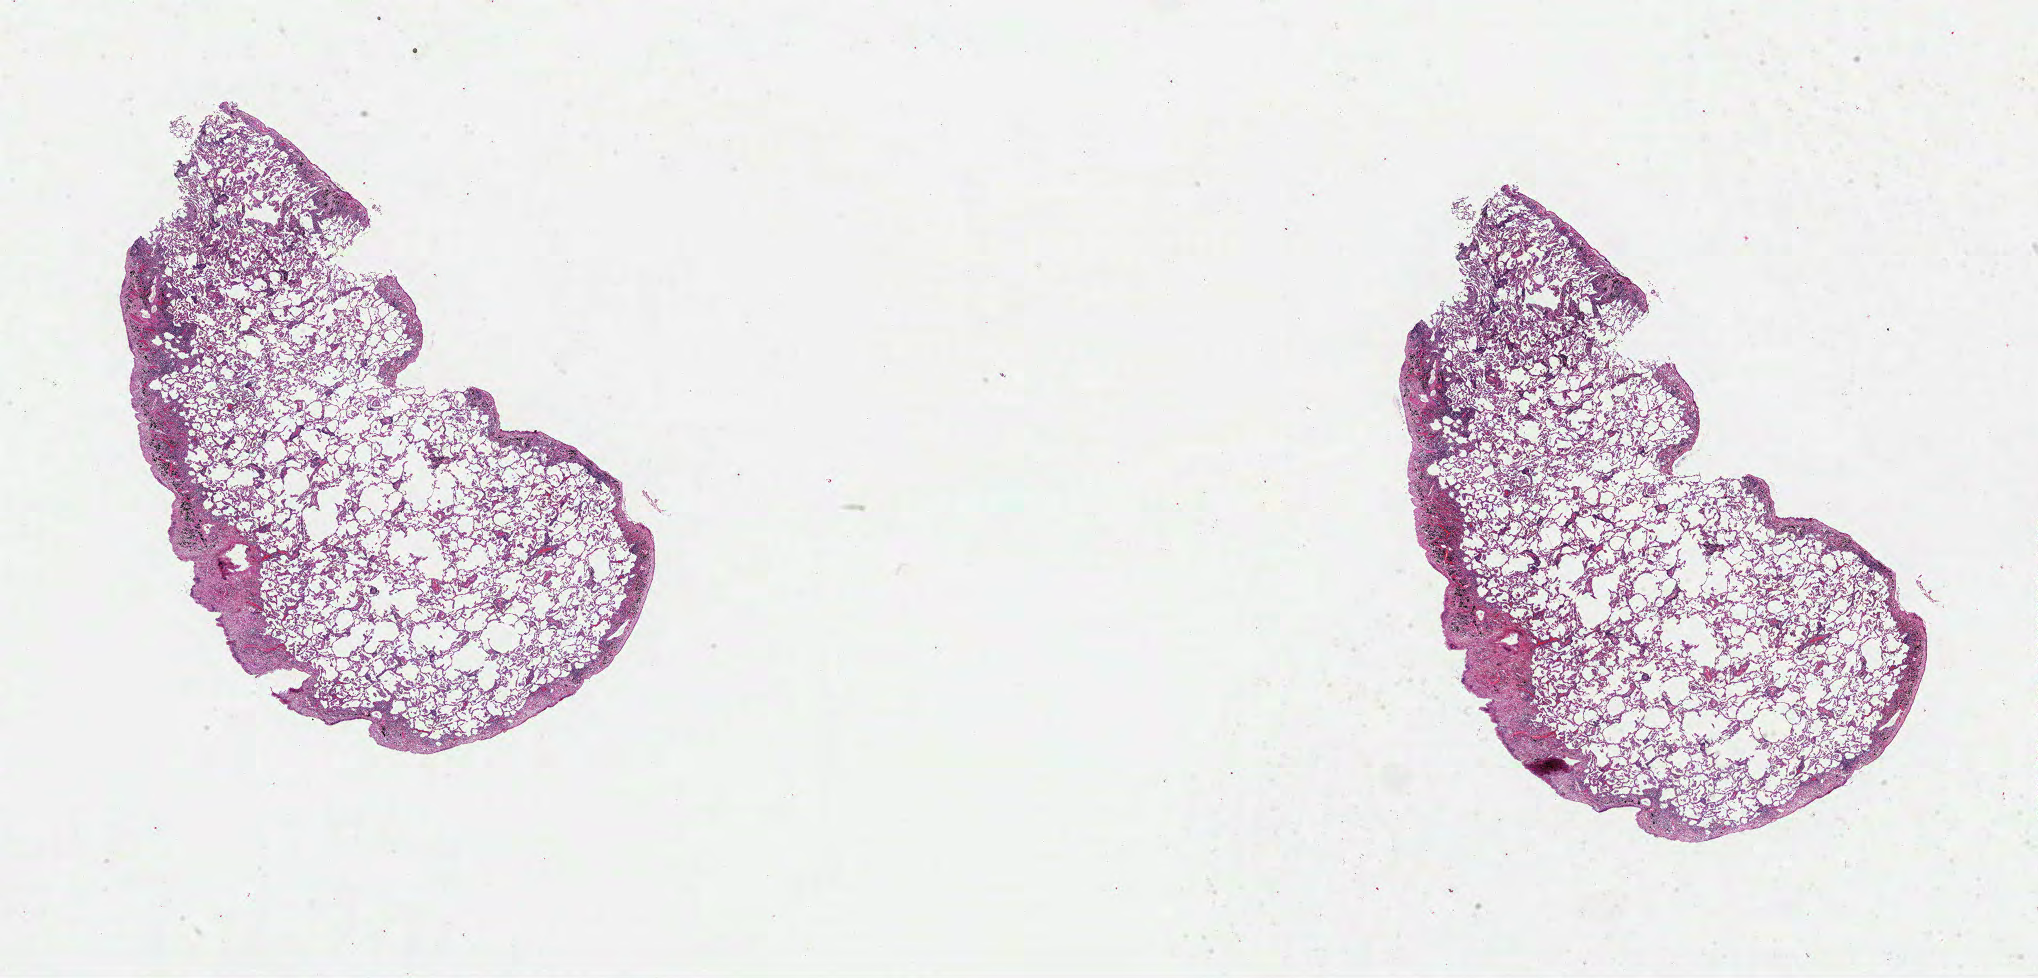
Digitized Hematoxylin and eosin (H&E) stained tissue section (whole slide) — whole scanned area (about 32.9 x 15.8 mm) shown as a low-resolution overview. FFPE section. Lung, primary tumour sample. Male patient; age at initial diagnosis 51 years.
TNM: T3 N2 M0. Laterality: left. Diagnosis: Squamous cell carcinoma, NOS (upper lobe, lung). AJCC pathologic stage: IIIA.